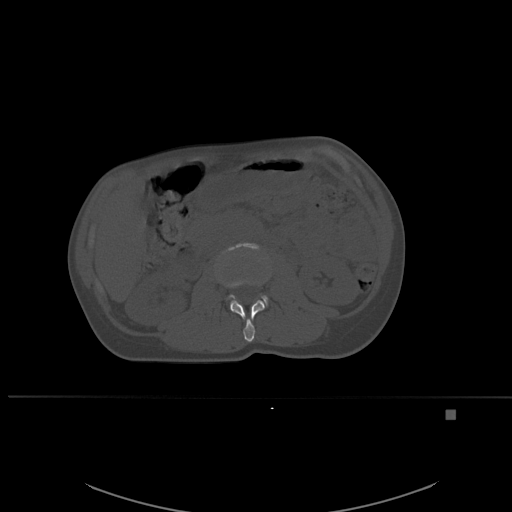
CT including the spine, one axial slice. Slice 227 of 537 in the series (ordered by position). Bone window (W 1800 / L 400 HU). 1.5 mm slice thickness. 512 × 512 image matrix, field of view 440 × 440 mm. Patient: female, 45 years. Case-level facts recorded for this patient, not image findings: primary cancer: lung.
Structures marked on this image (semi-automatic segmentation, software-assisted and operator-edited):
- L2 vertebra: bounding box [x1, y1, x2, y2] px = [221, 280, 265, 342]
- L3 vertebra: [216, 242, 268, 306]